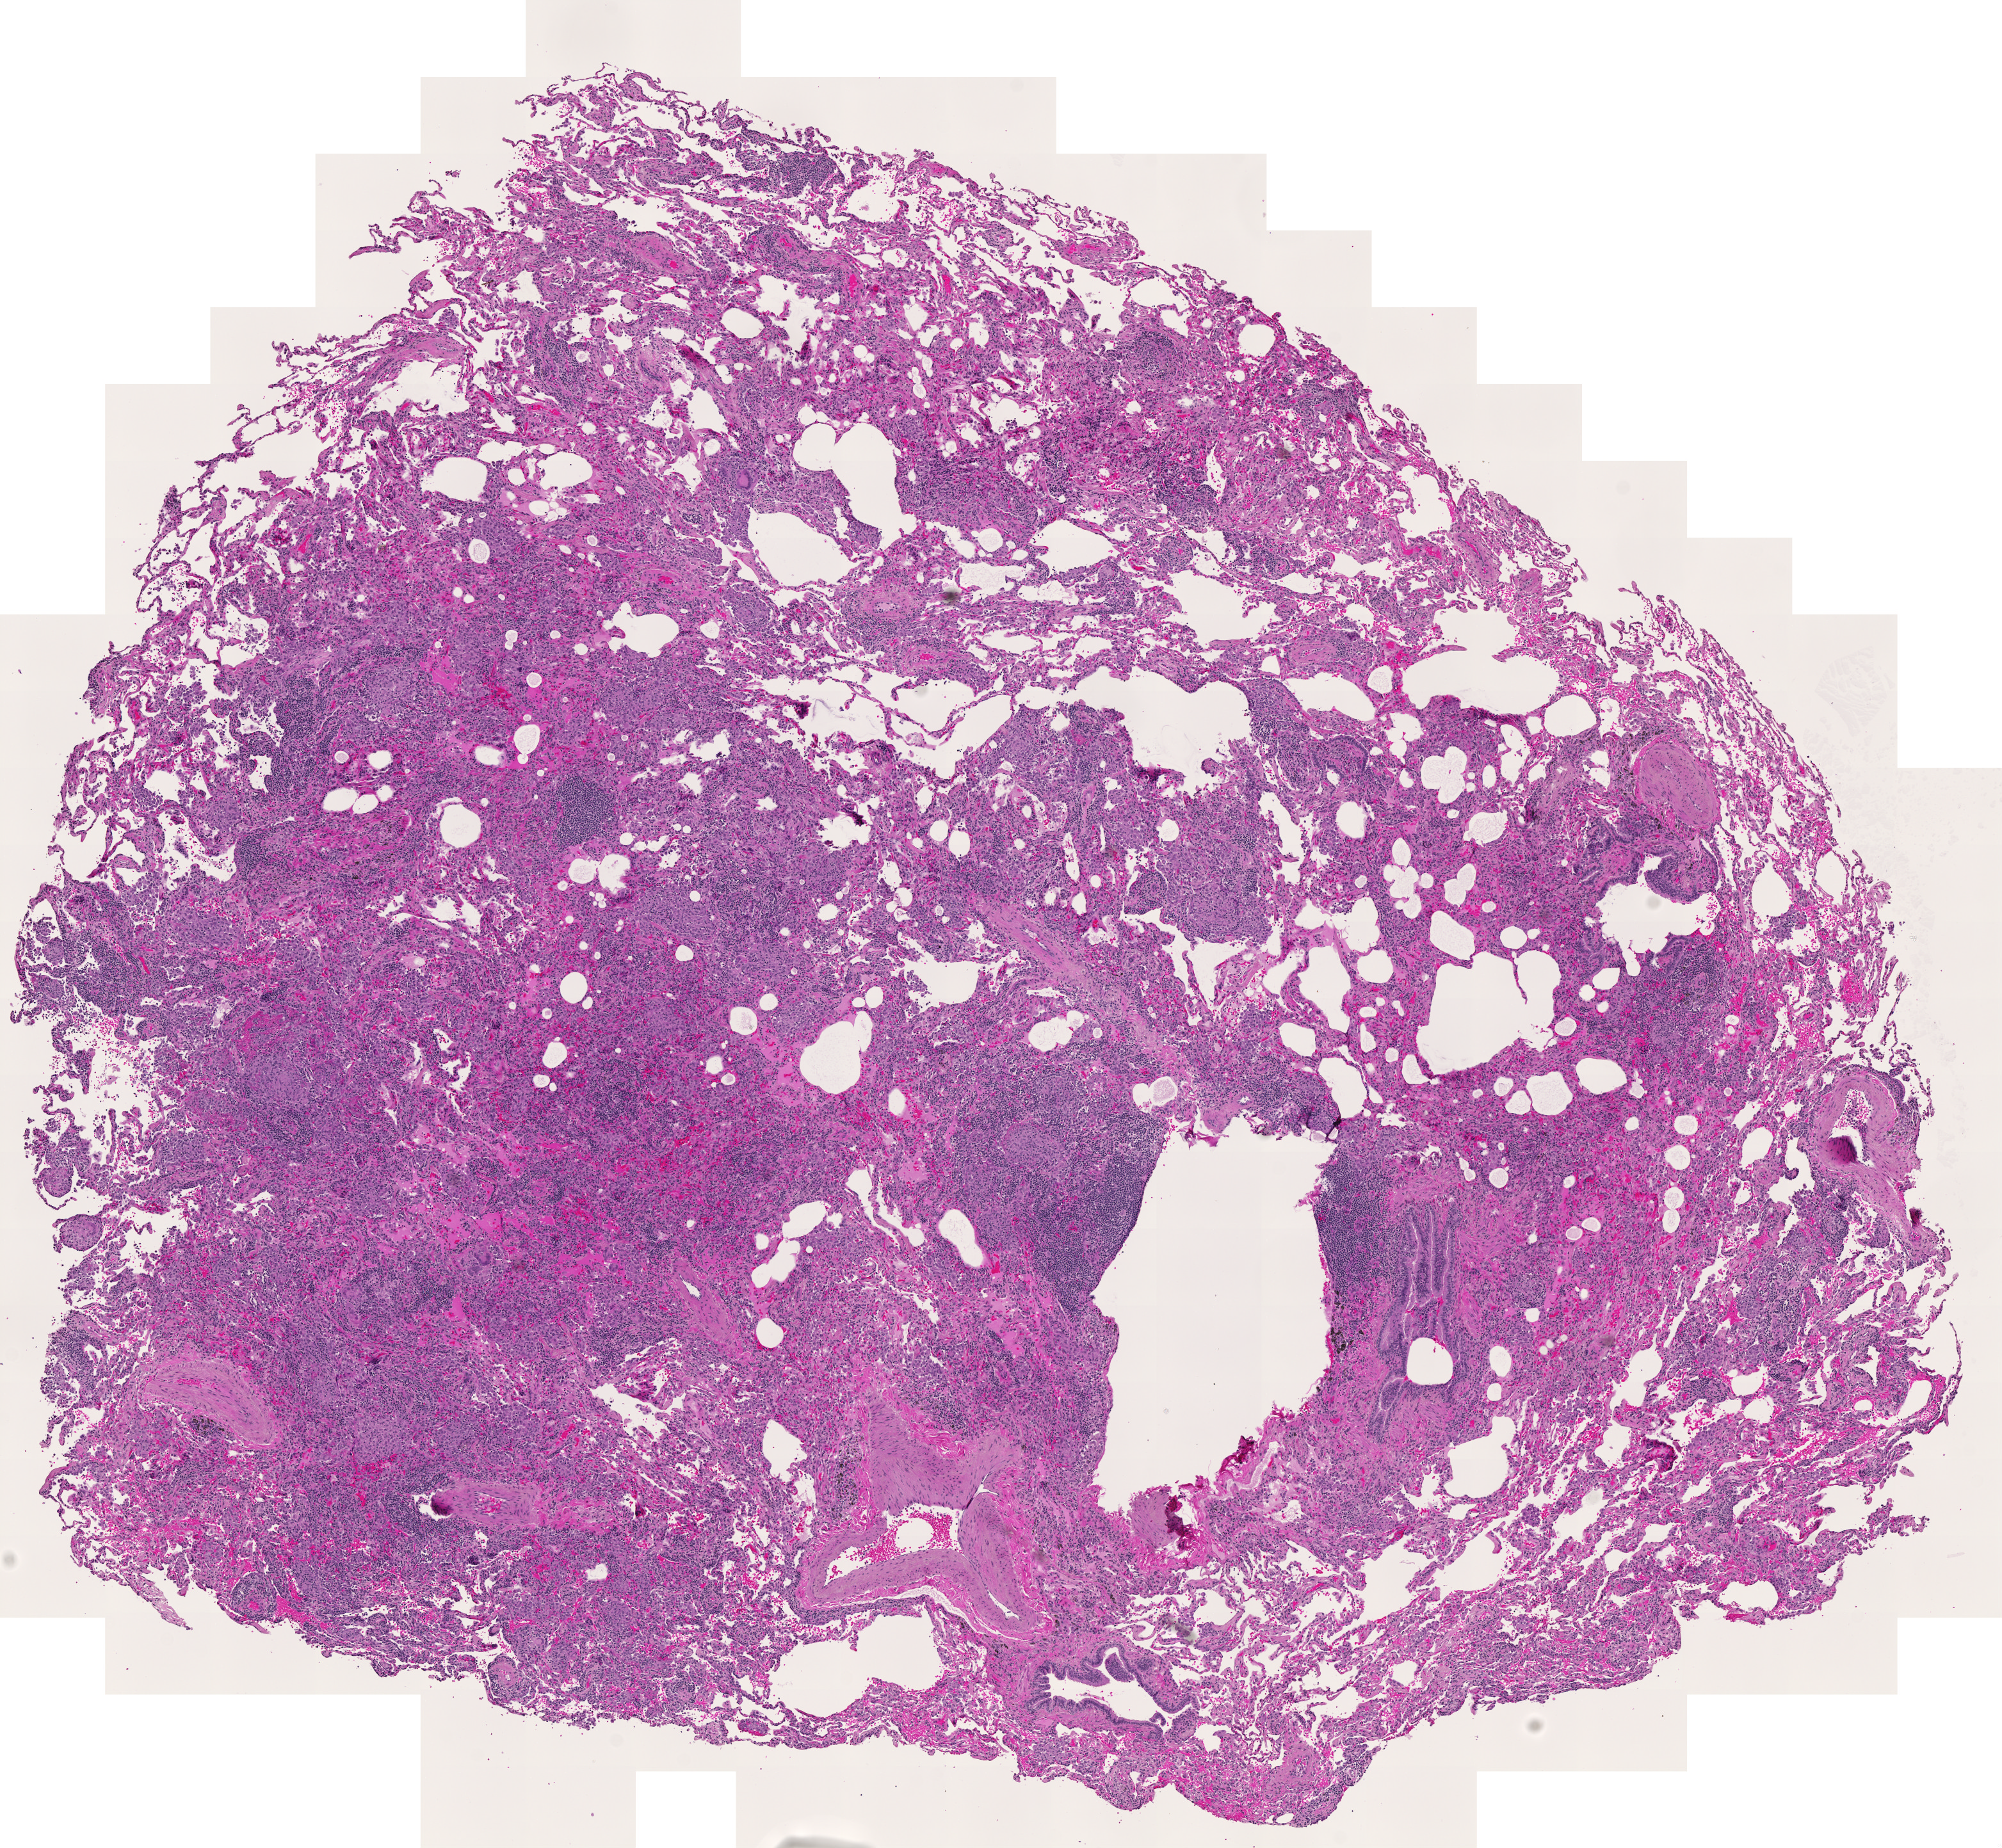
H&E whole-slide image — a low-resolution overview of the entire scanned area, about 8.1 x 7.5 mm; normal (non-tumour) tissue sample, sampled site: lung. Patient: male, age 73 years.
This section: normal (non-tumour) tissue from the same patient. Patient diagnosis: Adenocarcinoma, NOS.